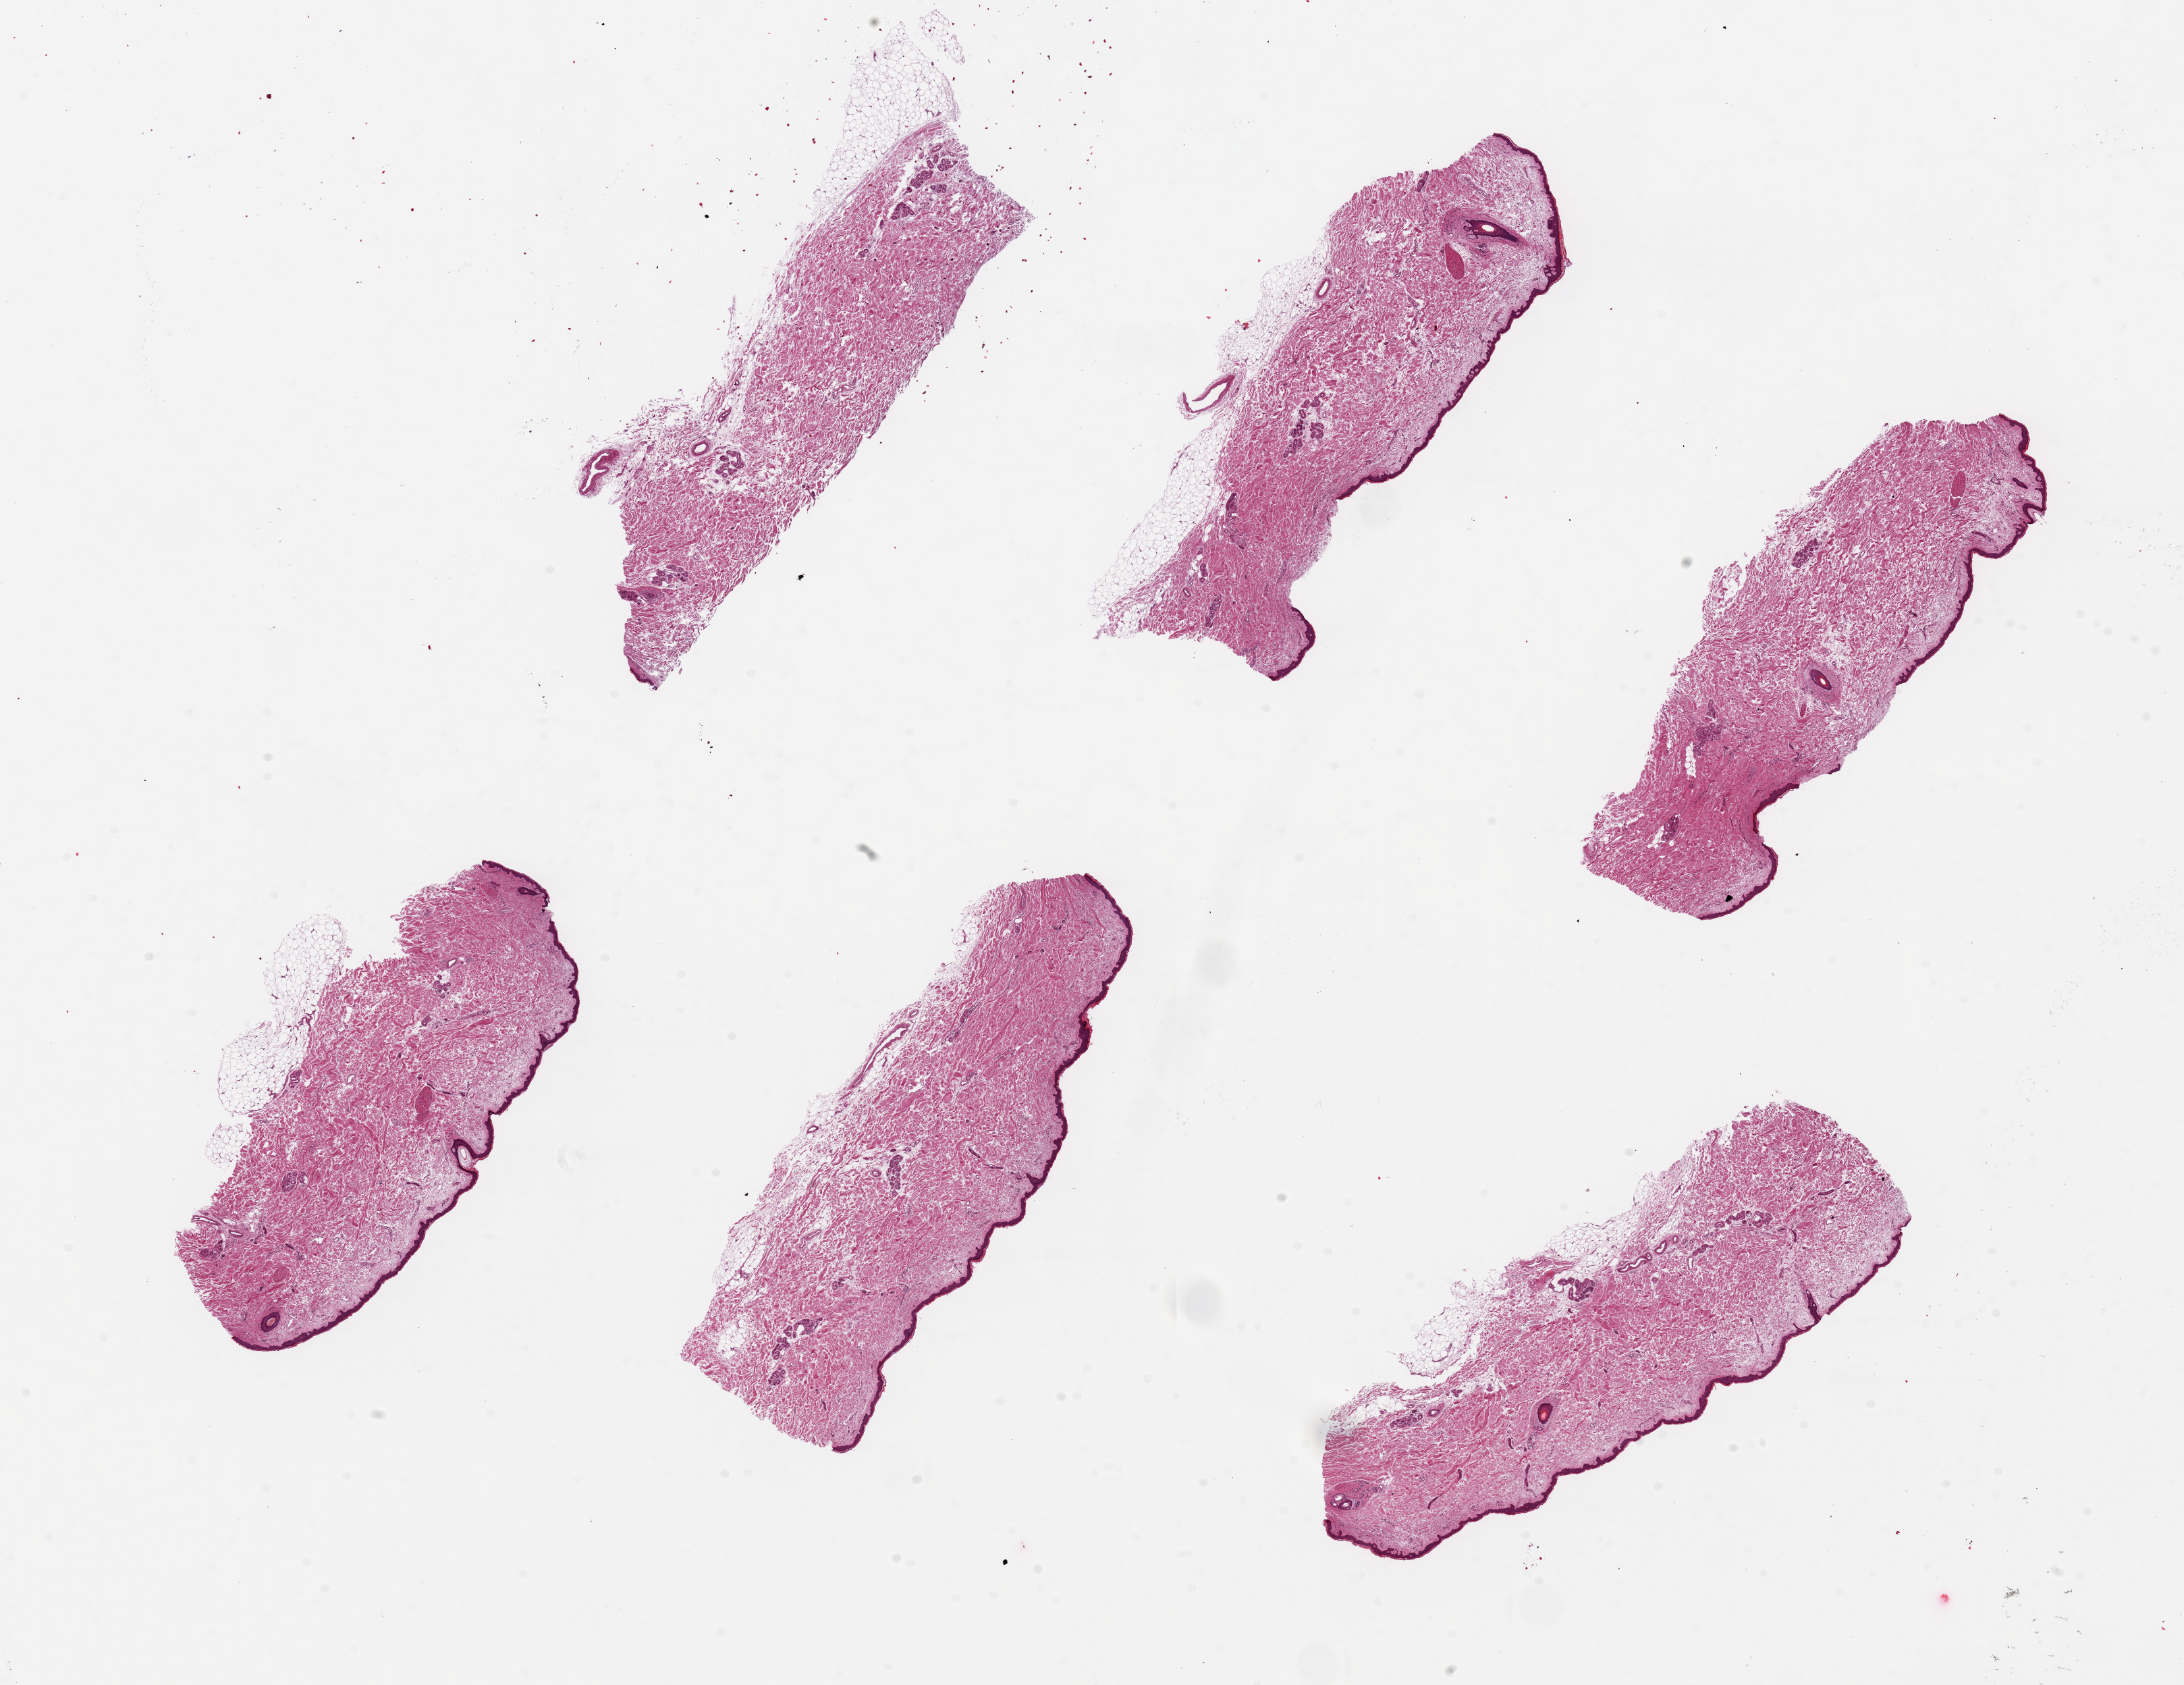
Digitized H&E-stained section, brightfield, low-resolution overview of the scanned area, about 25.6 x 19.7 mm; PAXgene-fixed paraffin-embedded (PFPE) section; section of skin of lower leg (target tissue); donor tissue sample. Donor: male.
Pathologist's review note for this sample: 6 pieces, up to 8x3mm; most subcutaneous adipose tissue trimmed.